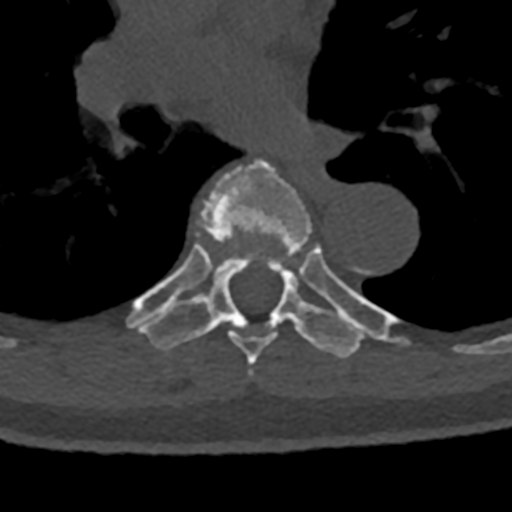
CT including the spine, one axial slice; position 783 of 797 along the scan axis; reconstruction kernel Br40s/3; 120 kVp; bone window (W 1800 / L 400 HU); 0.5 mm slice thickness; 512 × 512 image matrix, field of view 160 × 160 mm. Patient: male, 74 years. From the clinical record (not read from this slice): primary cancer: renal.
Outlined on this slice (semi-automatic segmentation, software-assisted and operator-edited):
- T6 vertebra: bounding box [x1, y1, x2, y2] px = [170, 158, 313, 365]
- T7 vertebra: [127, 244, 394, 359]